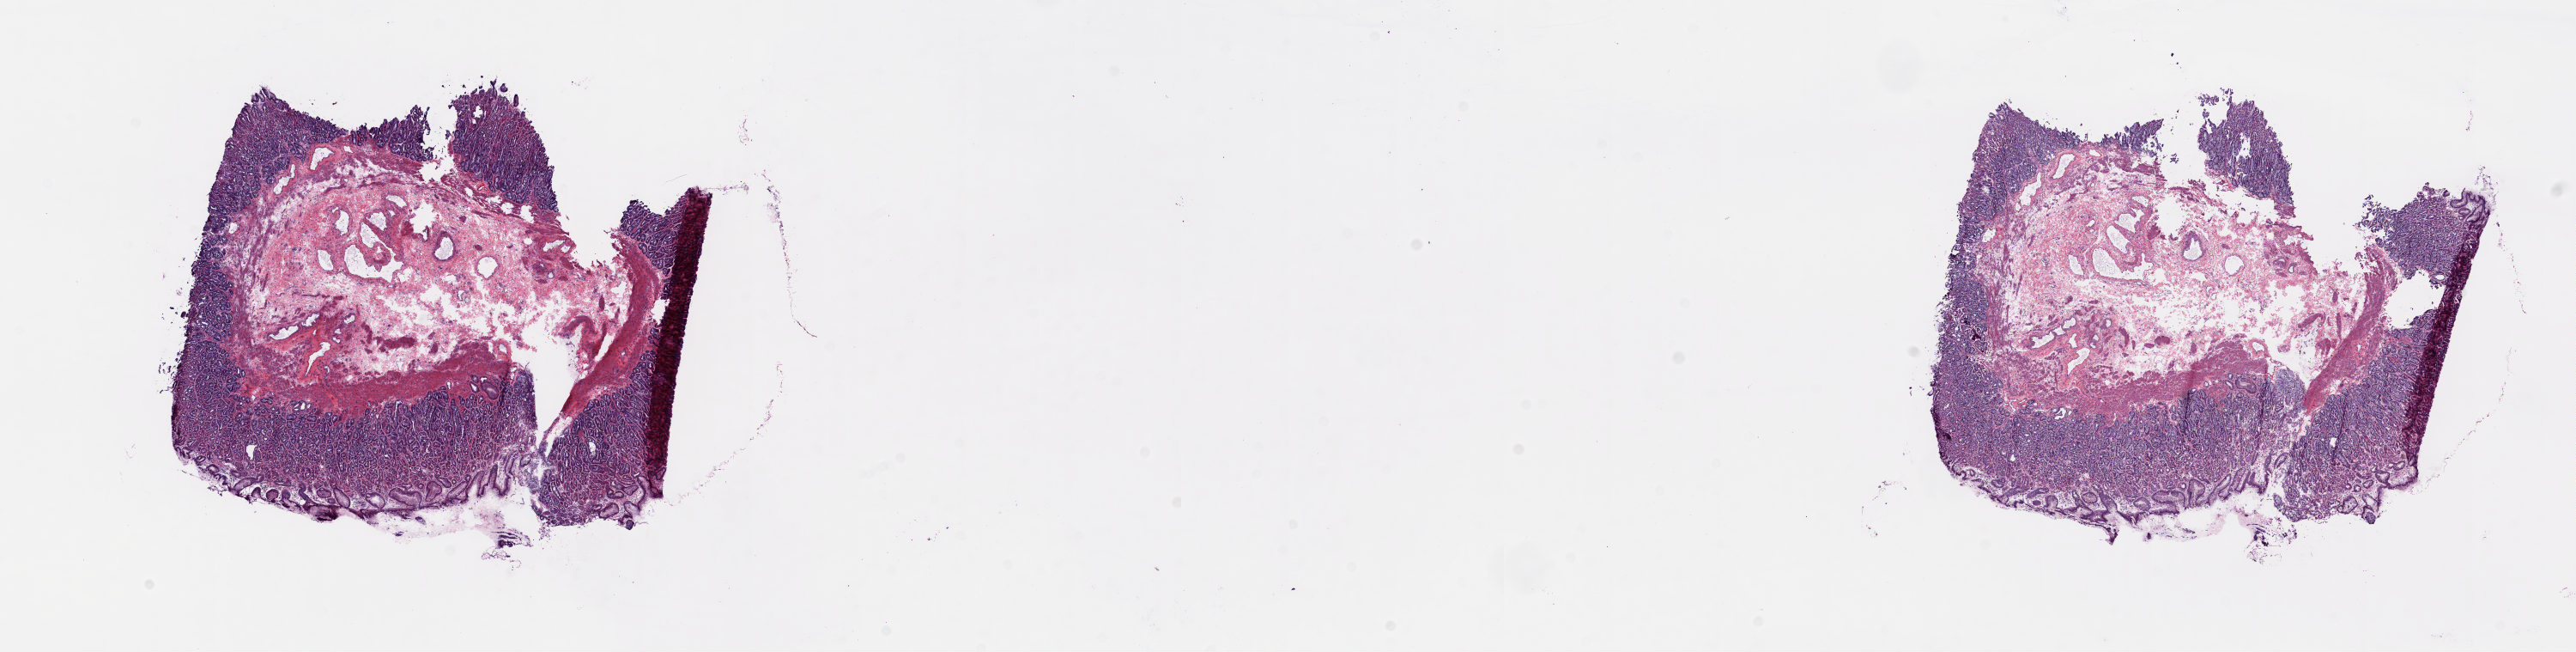
Whole-slide histology image, H&E, whole scanned area (about 23.8 x 6.0 mm, slide scanned at 20x) shown as a low-resolution overview; frozen section from the top of the tissue portion; esophagus, solid tissue normal (non-tumour tissue) sample. Patient: male, age at initial diagnosis 77 years.
This section: solid tissue normal (non-tumour) sample from the same patient. Patient diagnosis: Adenocarcinoma, NOS (lower third of esophagus).